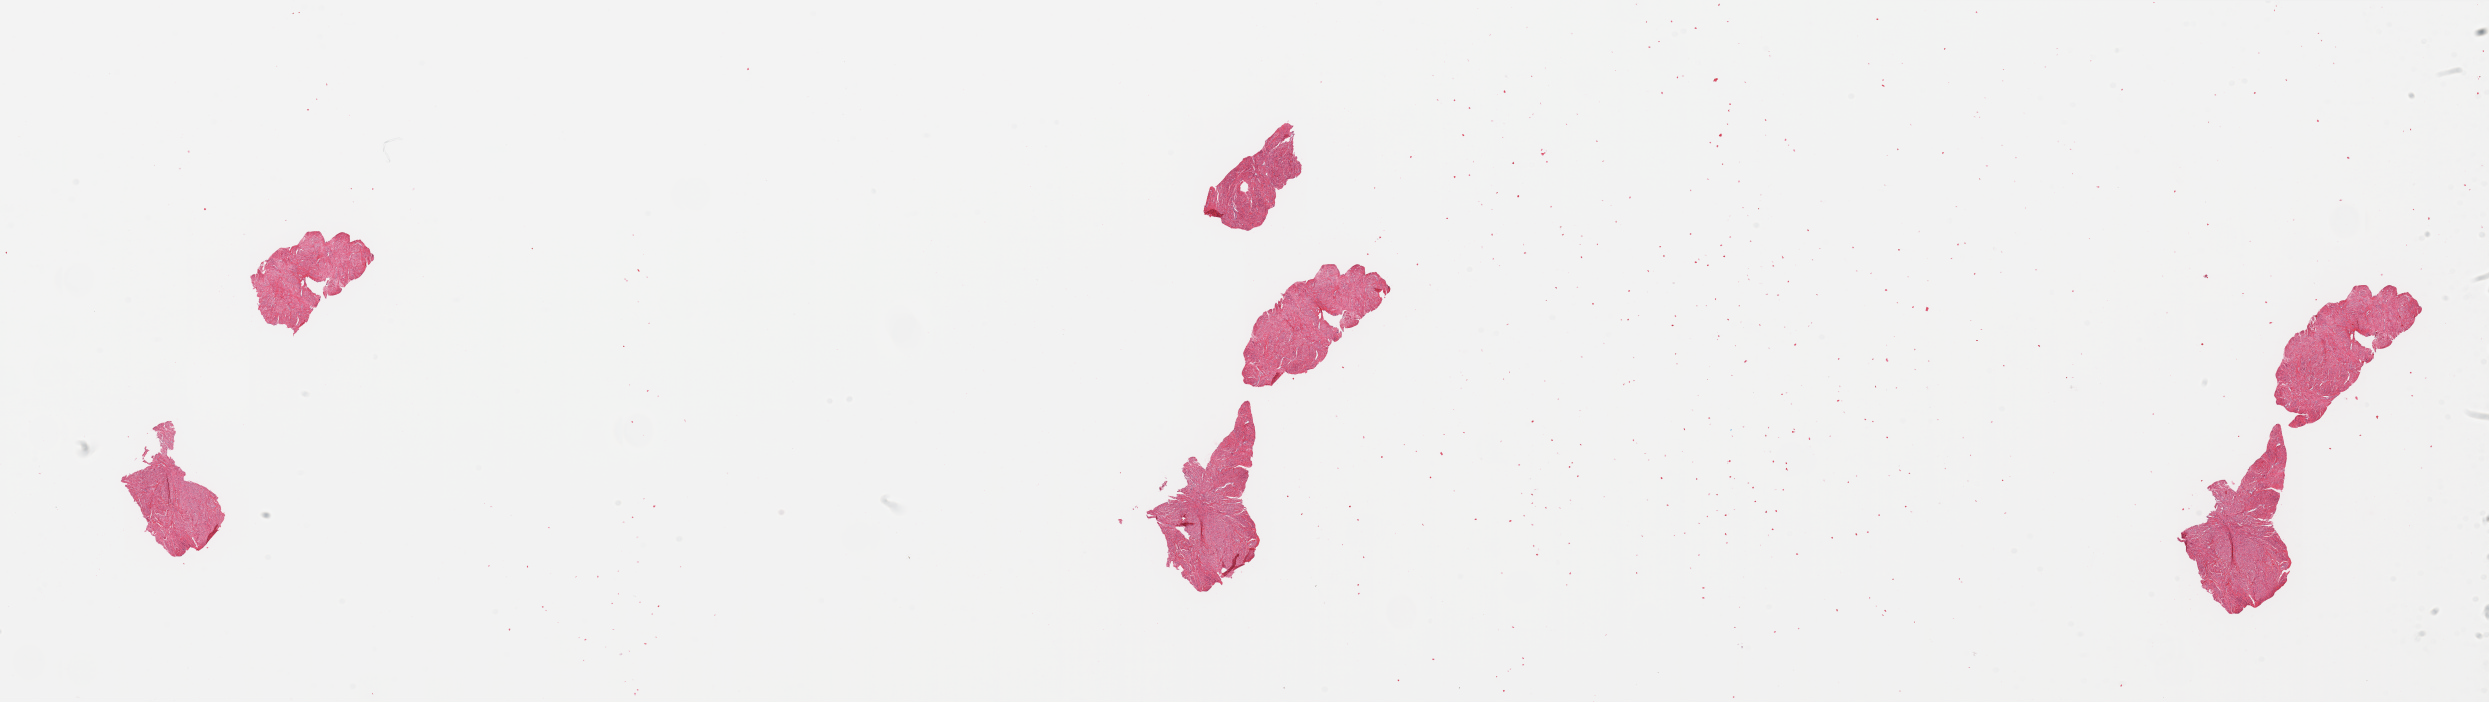
Digitized Hematoxylin and eosin (H&E) stained tissue section (whole slide), low-resolution overview of the scanned area, about 39.4 x 11.1 mm (slide scanned at 20x), uterus, normal (non-tumour) tissue. 72-year-old female patient.
This section: normal (non-tumour) tissue from the same patient. Patient diagnosis: Endometrioid adenocarcinoma, NOS.